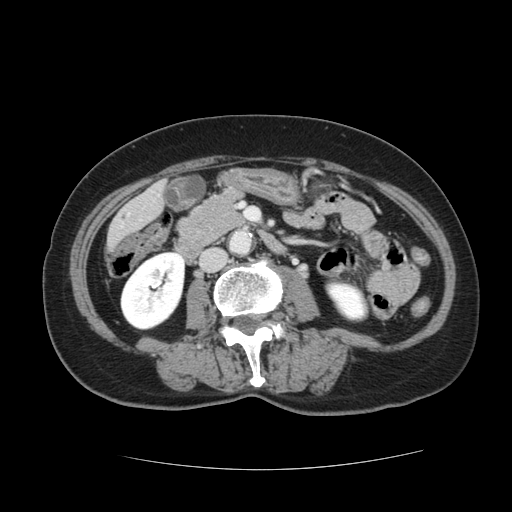
Contrast-enhanced abdominal CT, one axial slice; slice 23 of 128 in the series (ordered by position); 120 kVp; intravenous contrast given; soft-tissue window (W 400 / L 40 HU); 2.5 mm slice thickness; 512 × 512 image matrix. Female patient, age 67 years. From the clinical record (not read from this slice): diagnosis: colorectal cancer liver metastases, imaged before liver resection; multiple liver metastases: yes; largest metastasis: 3 cm.
Structures marked on this image (outlined manually by an expert reader):
- liver: bounding box <110,185,164,244> (left, top, right, bottom; pixels)
- planned liver remnant (the part of the liver to remain after resection): <110,208,141,244>